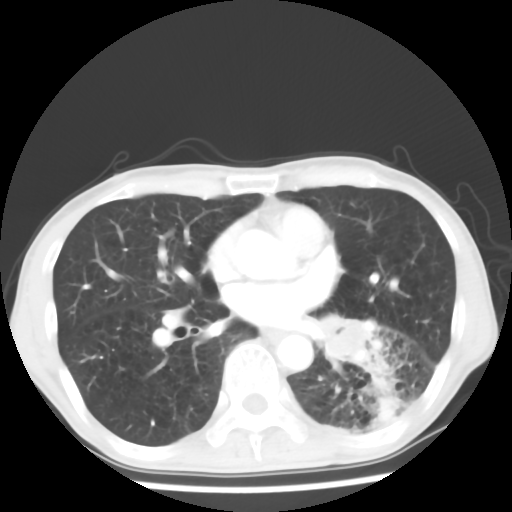
Chest CT, one axial slice. Position 30 of 64 along the scan axis. Reconstruction kernel STANDARD. 120 kVp. Lung window (W 1500 / L -600 HU). 512 × 512 image matrix. Patient: male, 68 years. Case-level facts recorded for this patient, not image findings: clinical TNM (as recorded): T4 N0 M0.
Annotated regions visible in this slice (bounding box drawn by a radiologist):
- lung tumour (recorded histology: squamous cell carcinoma): bounding box (x1, y1, x2, y2) in pixels: (311, 306, 381, 373)